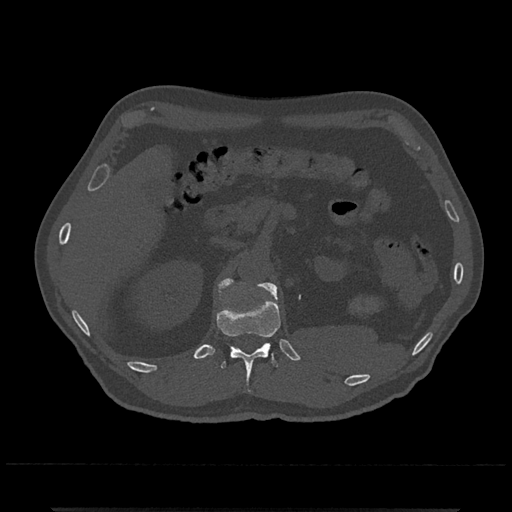
CT including the spine, one axial slice. Slice 416 of 797 in the series (ordered by position). Reconstruction kernel Br40s/3. Bone window (W 1800 / L 400 HU). 0.5 mm slice thickness. 512 × 512 image matrix, field of view 393 × 393 mm. Male patient, age 67 years. From the clinical record (not read from this slice): primary cancer: prostate.
Outlined on this slice (semi-automatically segmented with operator editing):
- L1 vertebra: bounding box <218,278,278,300> (left, top, right, bottom; pixels)
- T12 vertebra: <217,290,281,393>